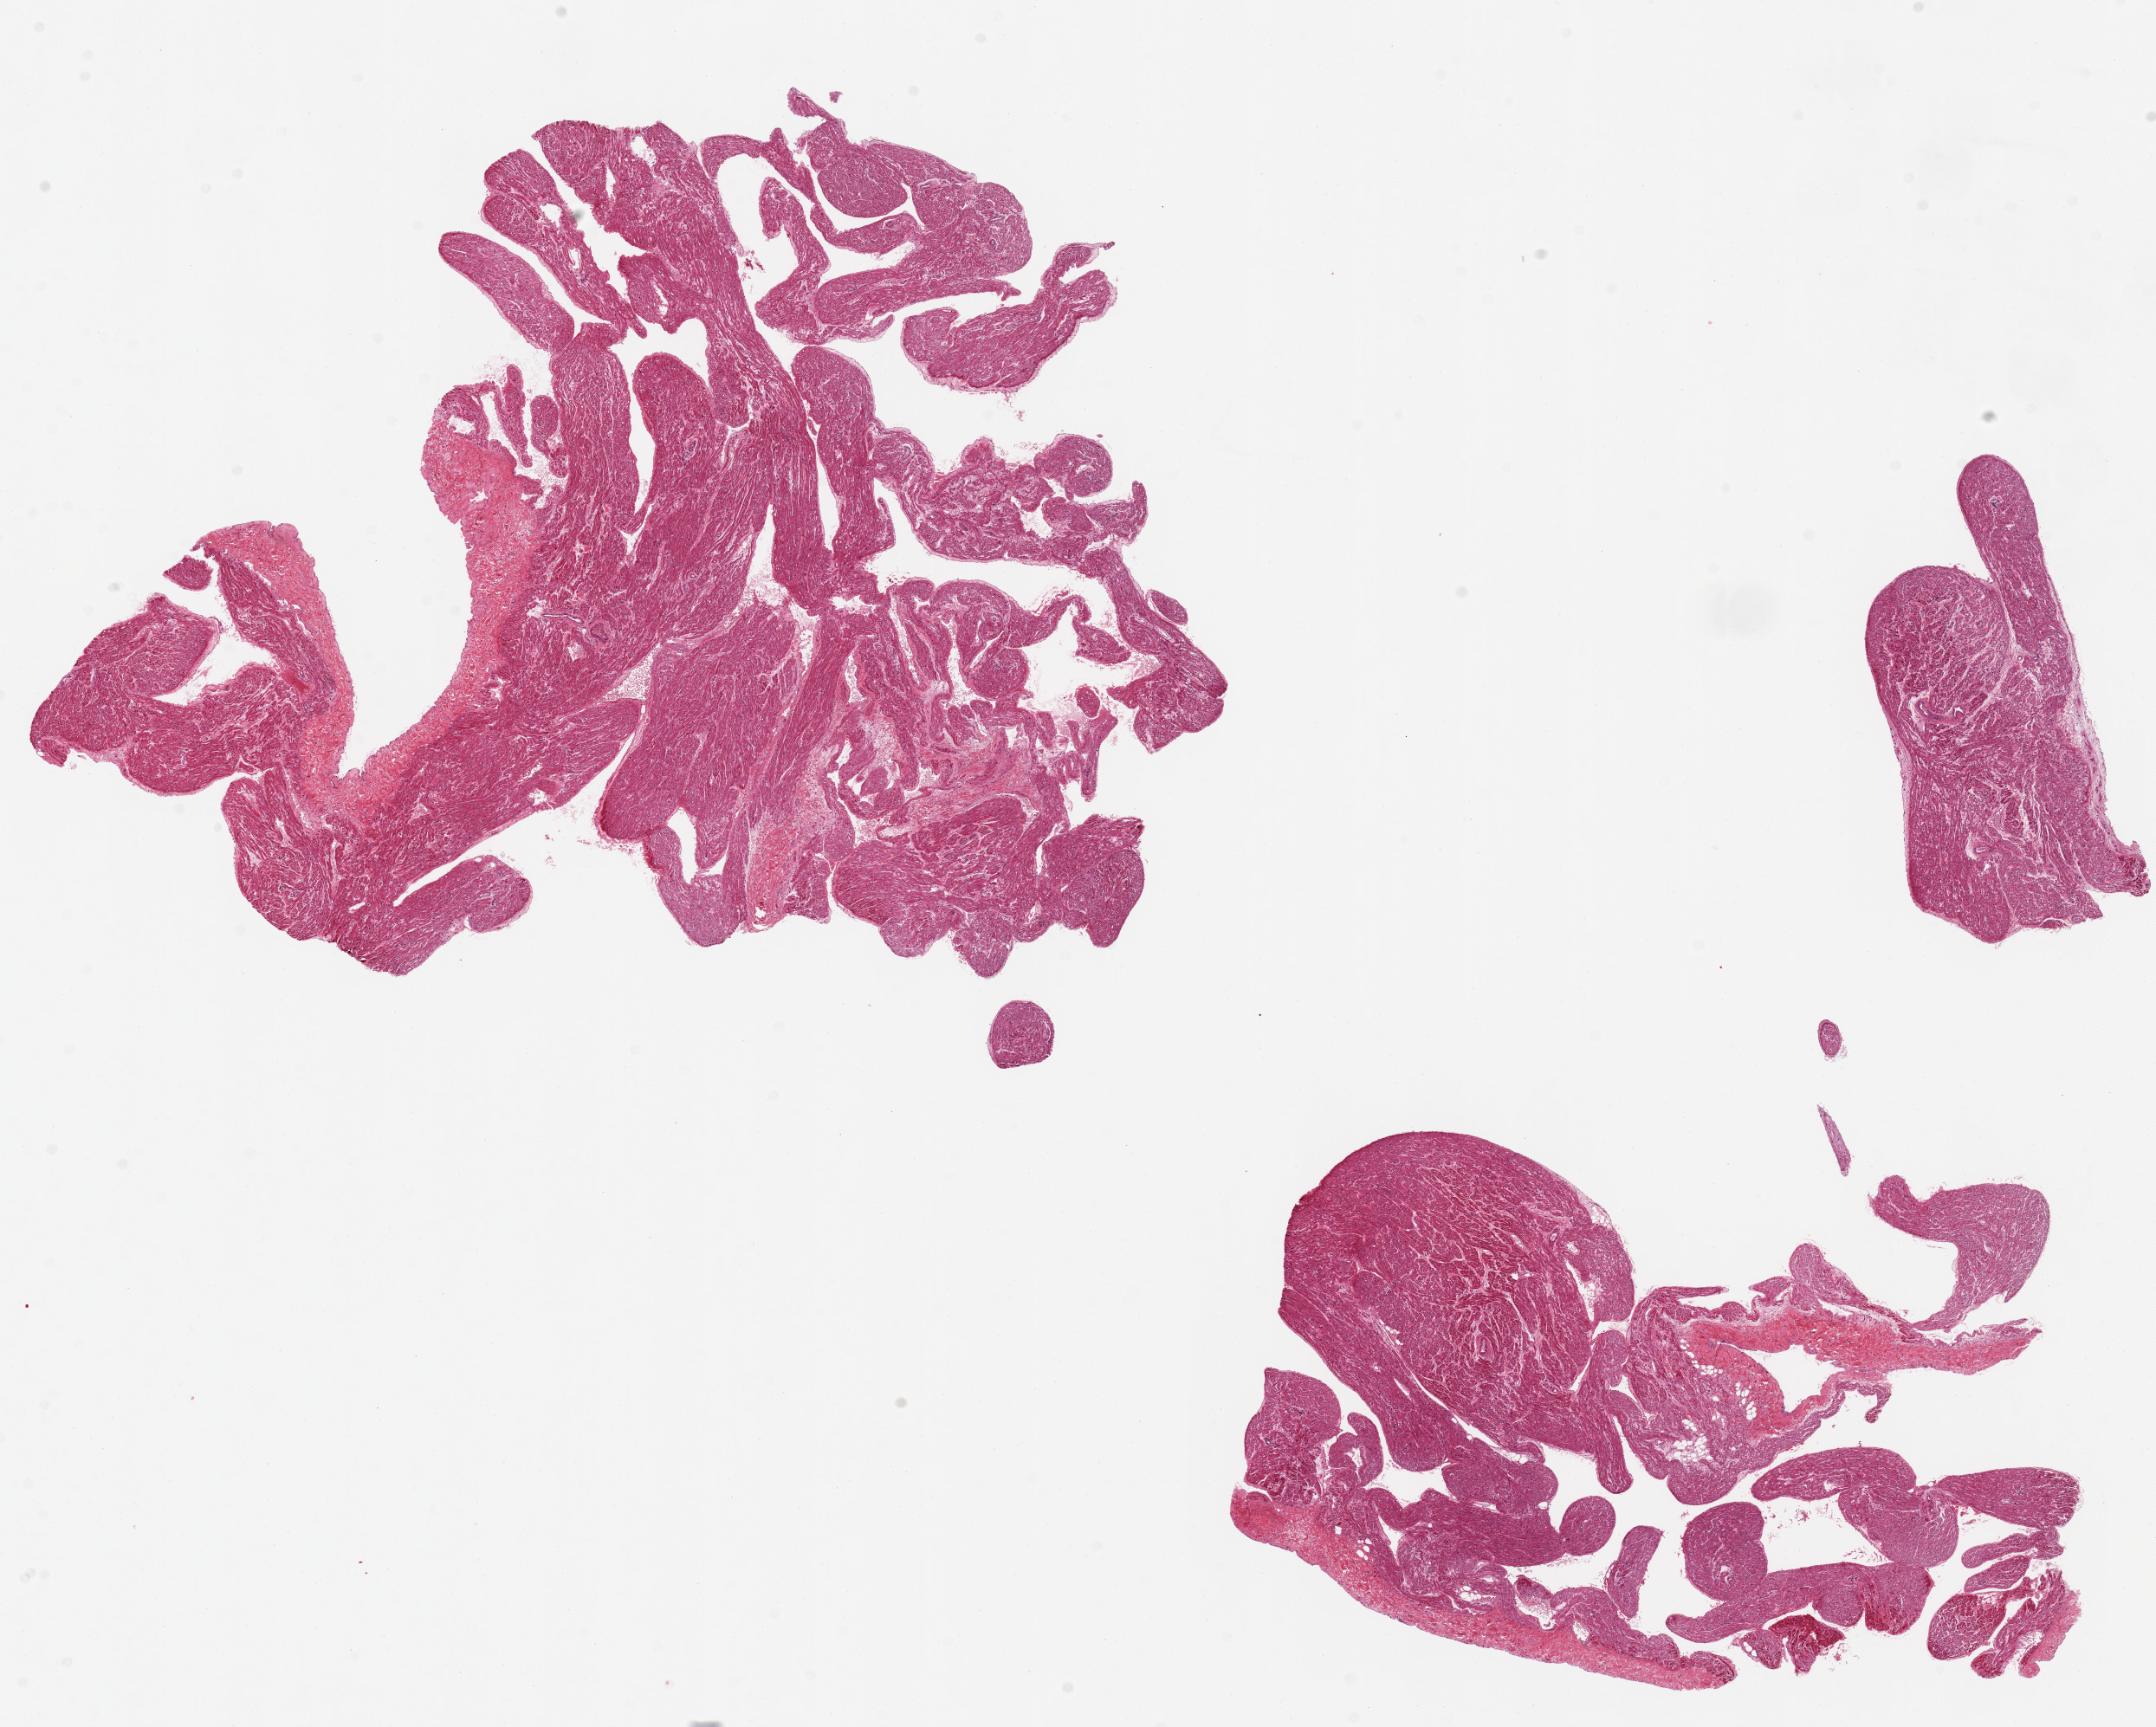
Digitized H&E-stained section, brightfield, a low-resolution overview of the entire scanned area, about 19.7 x 15.8 mm (acquisition: 20x scan), PAXgene-fixed paraffin-embedded (PFPE) section, target tissue: auricular appendage, tissue donor sample.
Review note (as recorded): 2 pieces, 10x10 & 11x7mm.